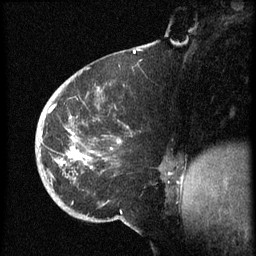
Breast MRI (dynamic contrast-enhanced), one sagittal slice; slice 22 of 60 in the series (ordered by position); dynamic contrast-enhanced series, image 2 of 3 at this slice position (ordered by acquisition); 1.5 T; TE 4.2 ms, TR 8.4 ms; 2.5 mm slice thickness; 256 × 256 image matrix, field of view 200 × 200 mm. Female patient, age 38 years. From the clinical record (not read from this slice): setting: breast cancer imaged before/during neoadjuvant chemotherapy; receptor status: HER2-positive.
Structures marked on this image (semi-automatic segmentation, software-assisted and operator-edited):
- analysis volume of interest (the breast-tissue region the enhancement analysis was run in; not a lesion): box from (x=36, y=74) to (x=173, y=202) px
- tumour enhancement mask (voxels above the 70 % enhancement threshold inside the analysis volume of interest): (x=41, y=105)–(x=120, y=169)